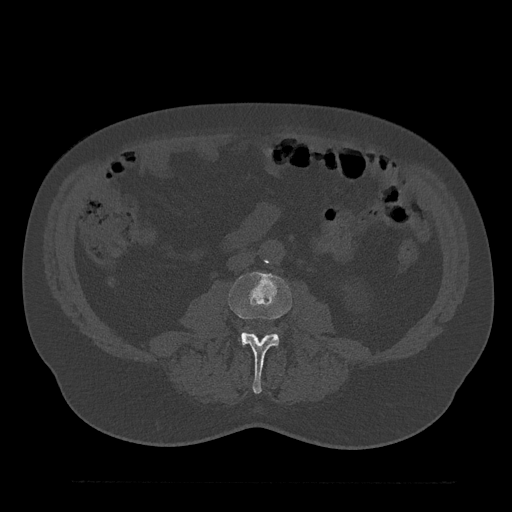
CT including the spine, one axial slice. Reconstruction kernel Br40s/3. 120 kVp. Bone window (W 1800 / L 400 HU). 0.5 mm slice thickness. 512 × 512 image matrix, field of view 430 × 430 mm. Male patient, age 61 years. Case-level facts recorded for this patient, not image findings: primary cancer: prostate.
Outlined on this slice (semi-automatically segmented with operator editing):
- L3 vertebra: bounding box [x1, y1, x2, y2] px = [228, 272, 292, 394]
- L4 vertebra: [241, 338, 243, 343]